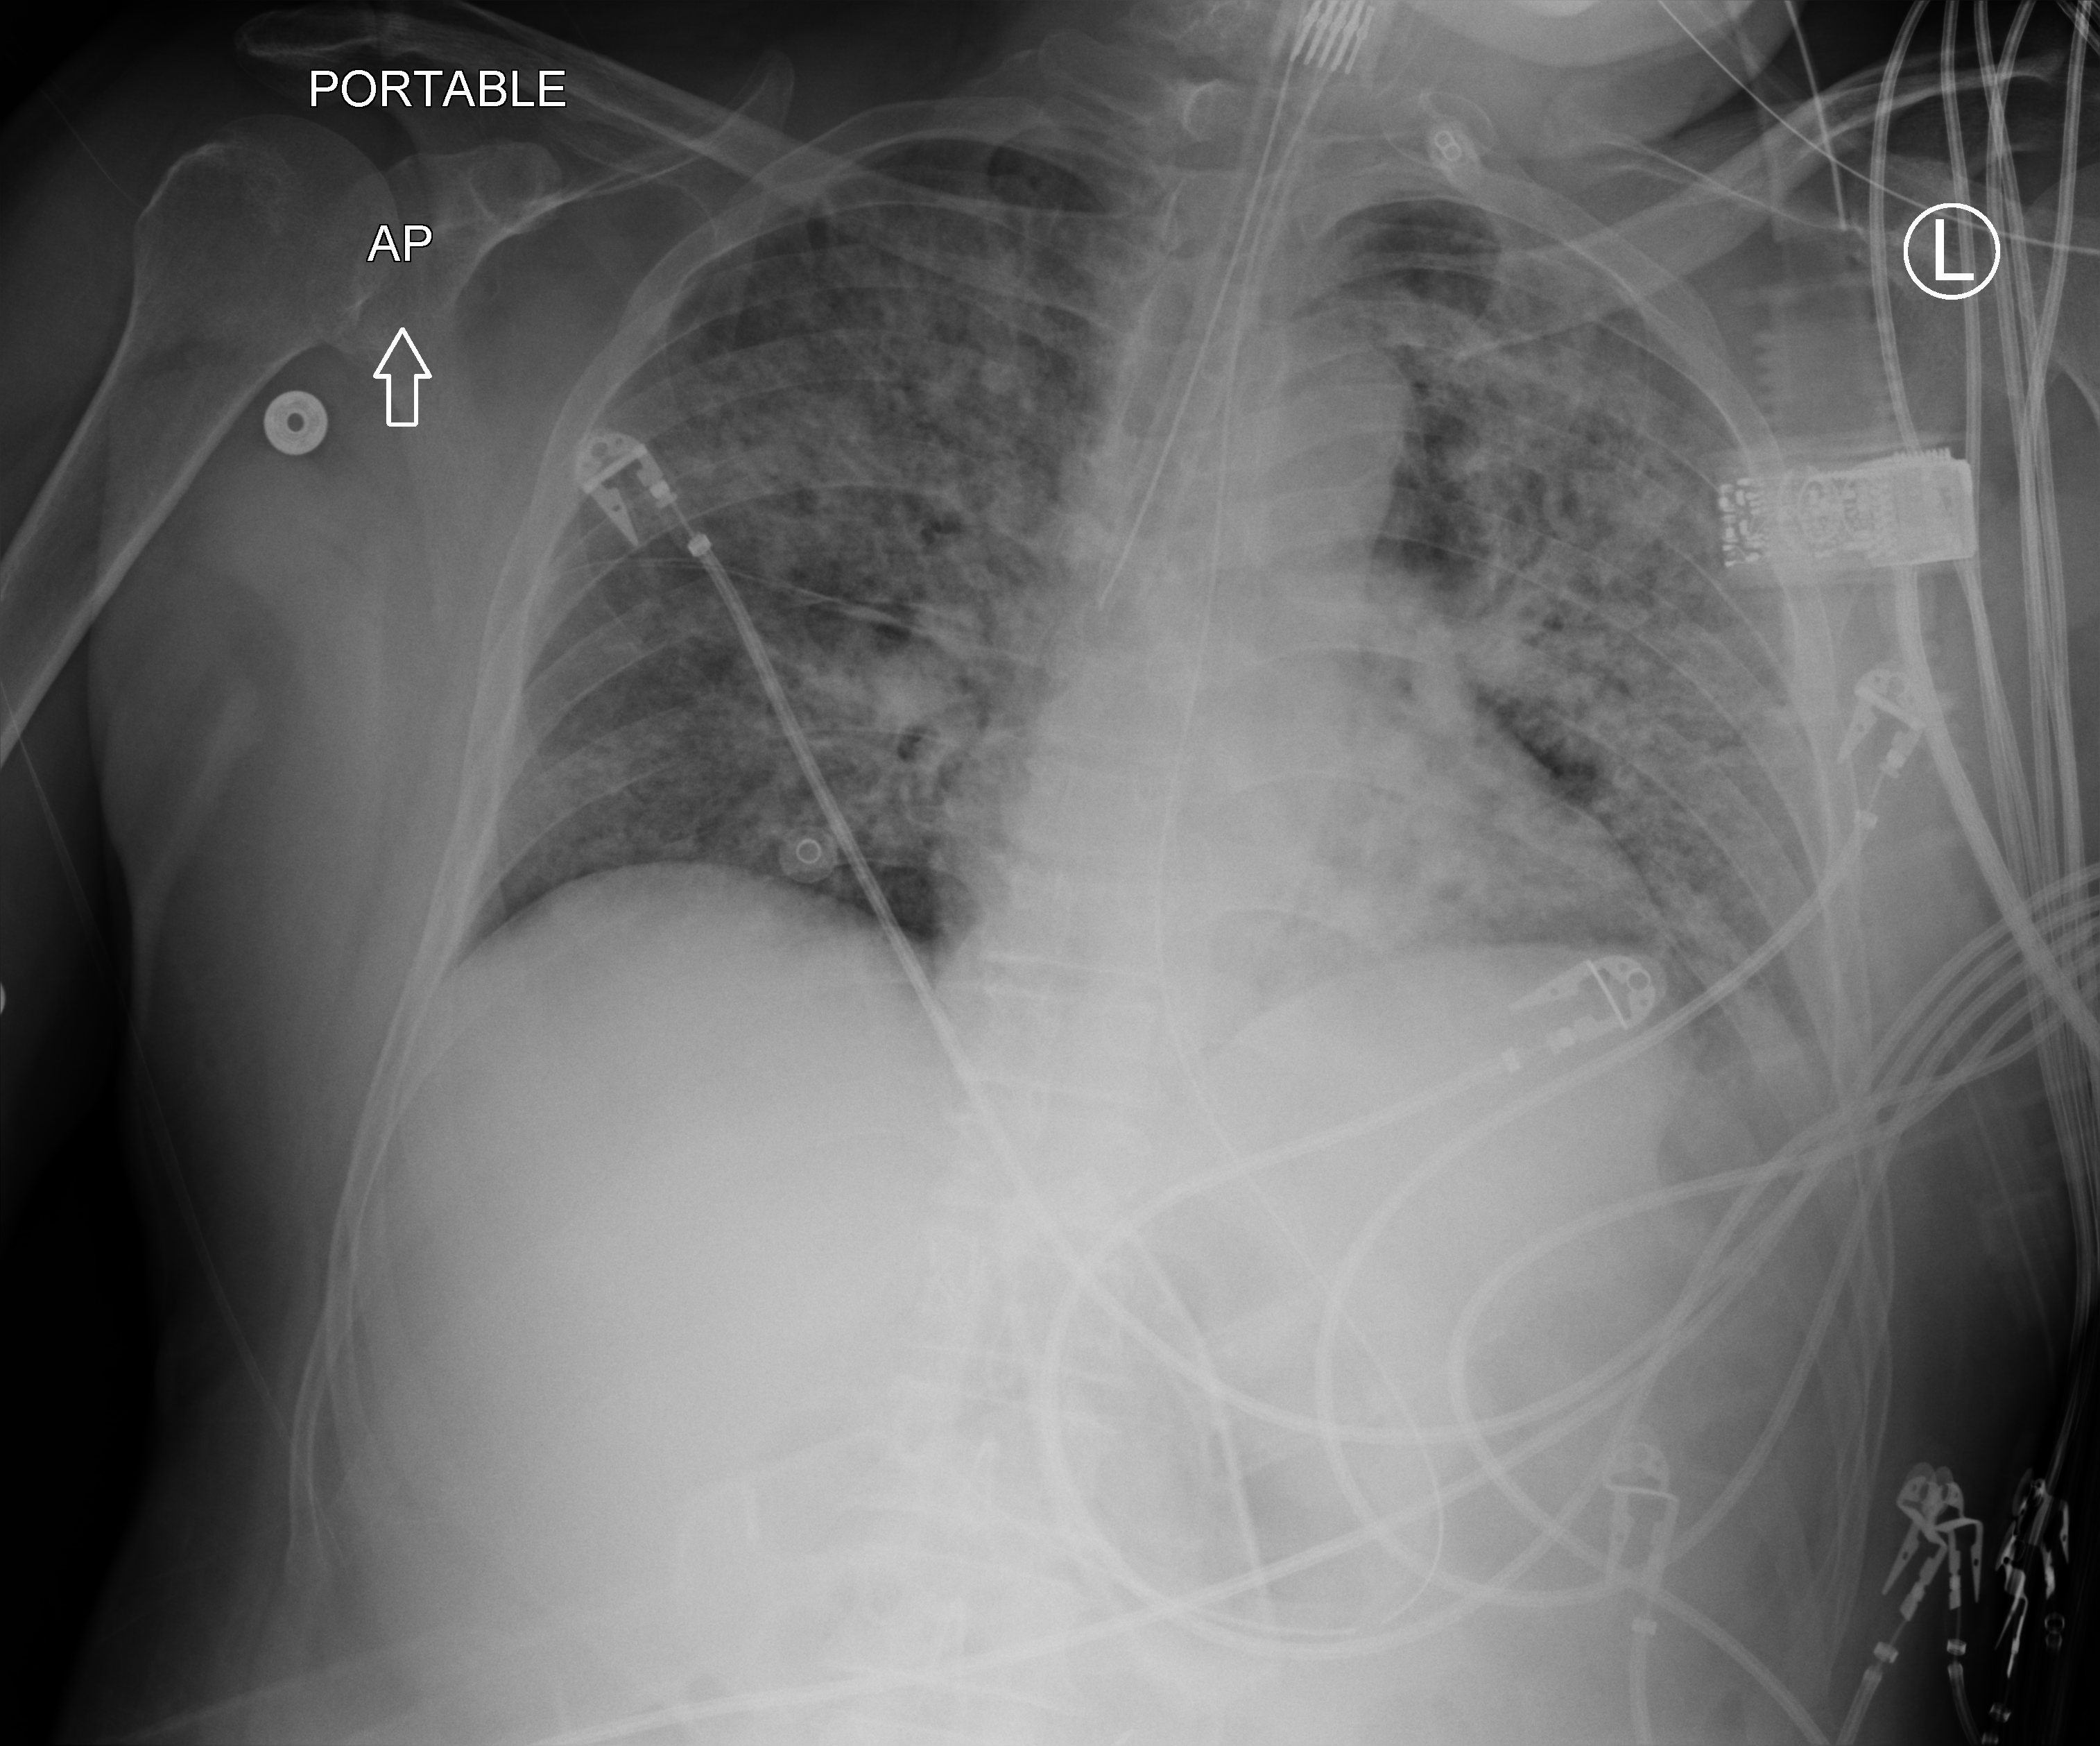
Chest X-ray (portable); anteroposterior (AP) projection. Male patient hospitalised with COVID-19, age 60–74 years.
Hospital-stay facts (about this admission, not read from this image; timing relative to this image not recorded):
- mechanically ventilated during this hospital stay: yes
- COPD (admission record): no
- admitted to intensive care during this hospital stay: yes